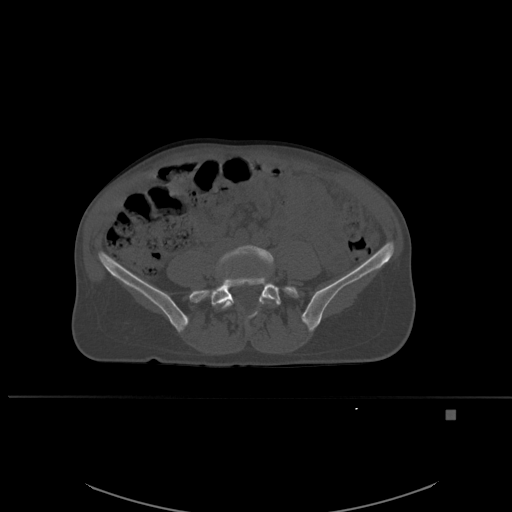
CT including the spine, one axial slice. Bone window (W 1800 / L 400 HU). 512 × 512 image matrix, field of view 440 × 440 mm. Patient: female, 45 years. Case-level facts recorded for this patient, not image findings: primary cancer: lung.
Outlined on this slice (semi-automatic segmentation, software-assisted and operator-edited):
- L4 vertebra: bounding box [x1, y1, x2, y2] px = [216, 245, 277, 309]
- L5 vertebra: [196, 272, 298, 317]